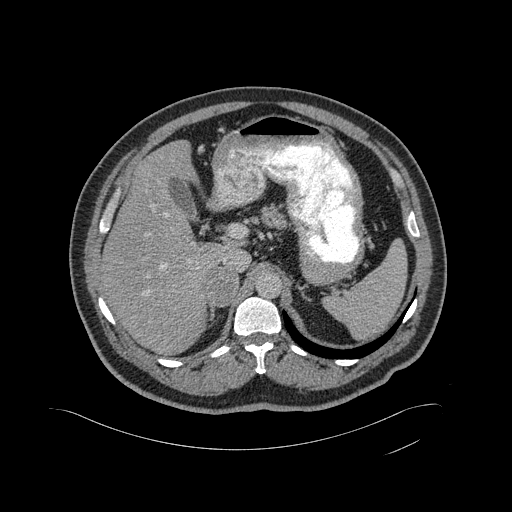
Contrast-enhanced abdominal CT, one axial slice. Position 327 of 433 along the scan axis. 120 kVp. Intravenous contrast given. Soft-tissue window (W 400 / L 40 HU). 512 × 512 image matrix, field of view 500 × 500 mm. Male patient, age 56 years. From the clinical record (not read from this slice): diagnosis: adrenocortical carcinoma; tumour side: right adrenal; tumour size at pathology: 11.6 cm; Ki-67 index: 50 %; stage (as recorded): 3.
Annotated regions visible in this slice (semi-automatic segmentation, software-assisted and operator-edited):
- mass: bounding box [x1, y1, x2, y2] px = [207, 268, 238, 305]